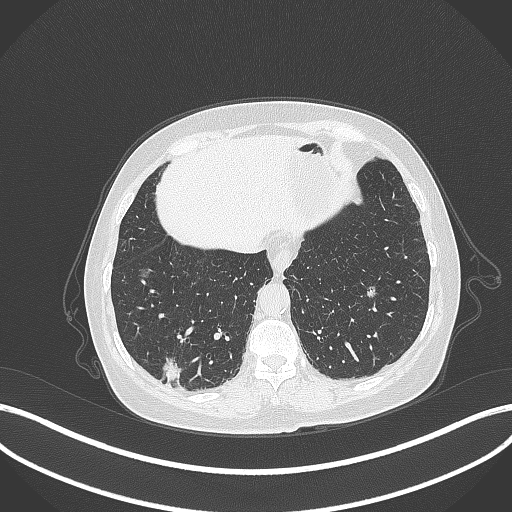
Chest CT, one axial slice. Position 66 of 333 along the scan axis. Reconstruction kernel B70f. 120 kVp. Lung window (W 1500 / L -600 HU). 1 mm slice thickness. 512 × 512 image matrix, field of view 400 × 400 mm. Female patient, age 69 years. From the clinical record (not read from this slice): clinical TNM (as recorded): T1b N0 M0.
Annotated regions visible in this slice (bounding box drawn by a radiologist):
- lung tumour (recorded histology: adenocarcinoma): bounding box [x1, y1, x2, y2] px = [162, 355, 184, 381]